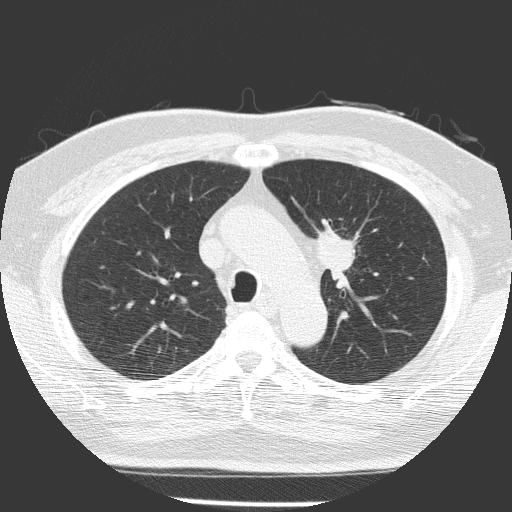
Axial slice from a low-dose chest CT screening exam, baseline annual screen, lung window (W 1500 / L -600 HU), 2 mm slice thickness, lung (sharp) reconstruction kernel (FC51), 512 × 512 image matrix, field of view 309 × 309 mm. Male, age 70 years at enrolment. Current smoker at enrolment.
Expert-annotated lung lesion, bounding box [x1, y1, x2, y2] px = [299, 224, 372, 299]. The screening reader recorded 3 non-calcified nodules or masses ≥4 mm on this exam (left upper lobe, left lower lobe, left upper lobe); which of them this box marks is not recorded.